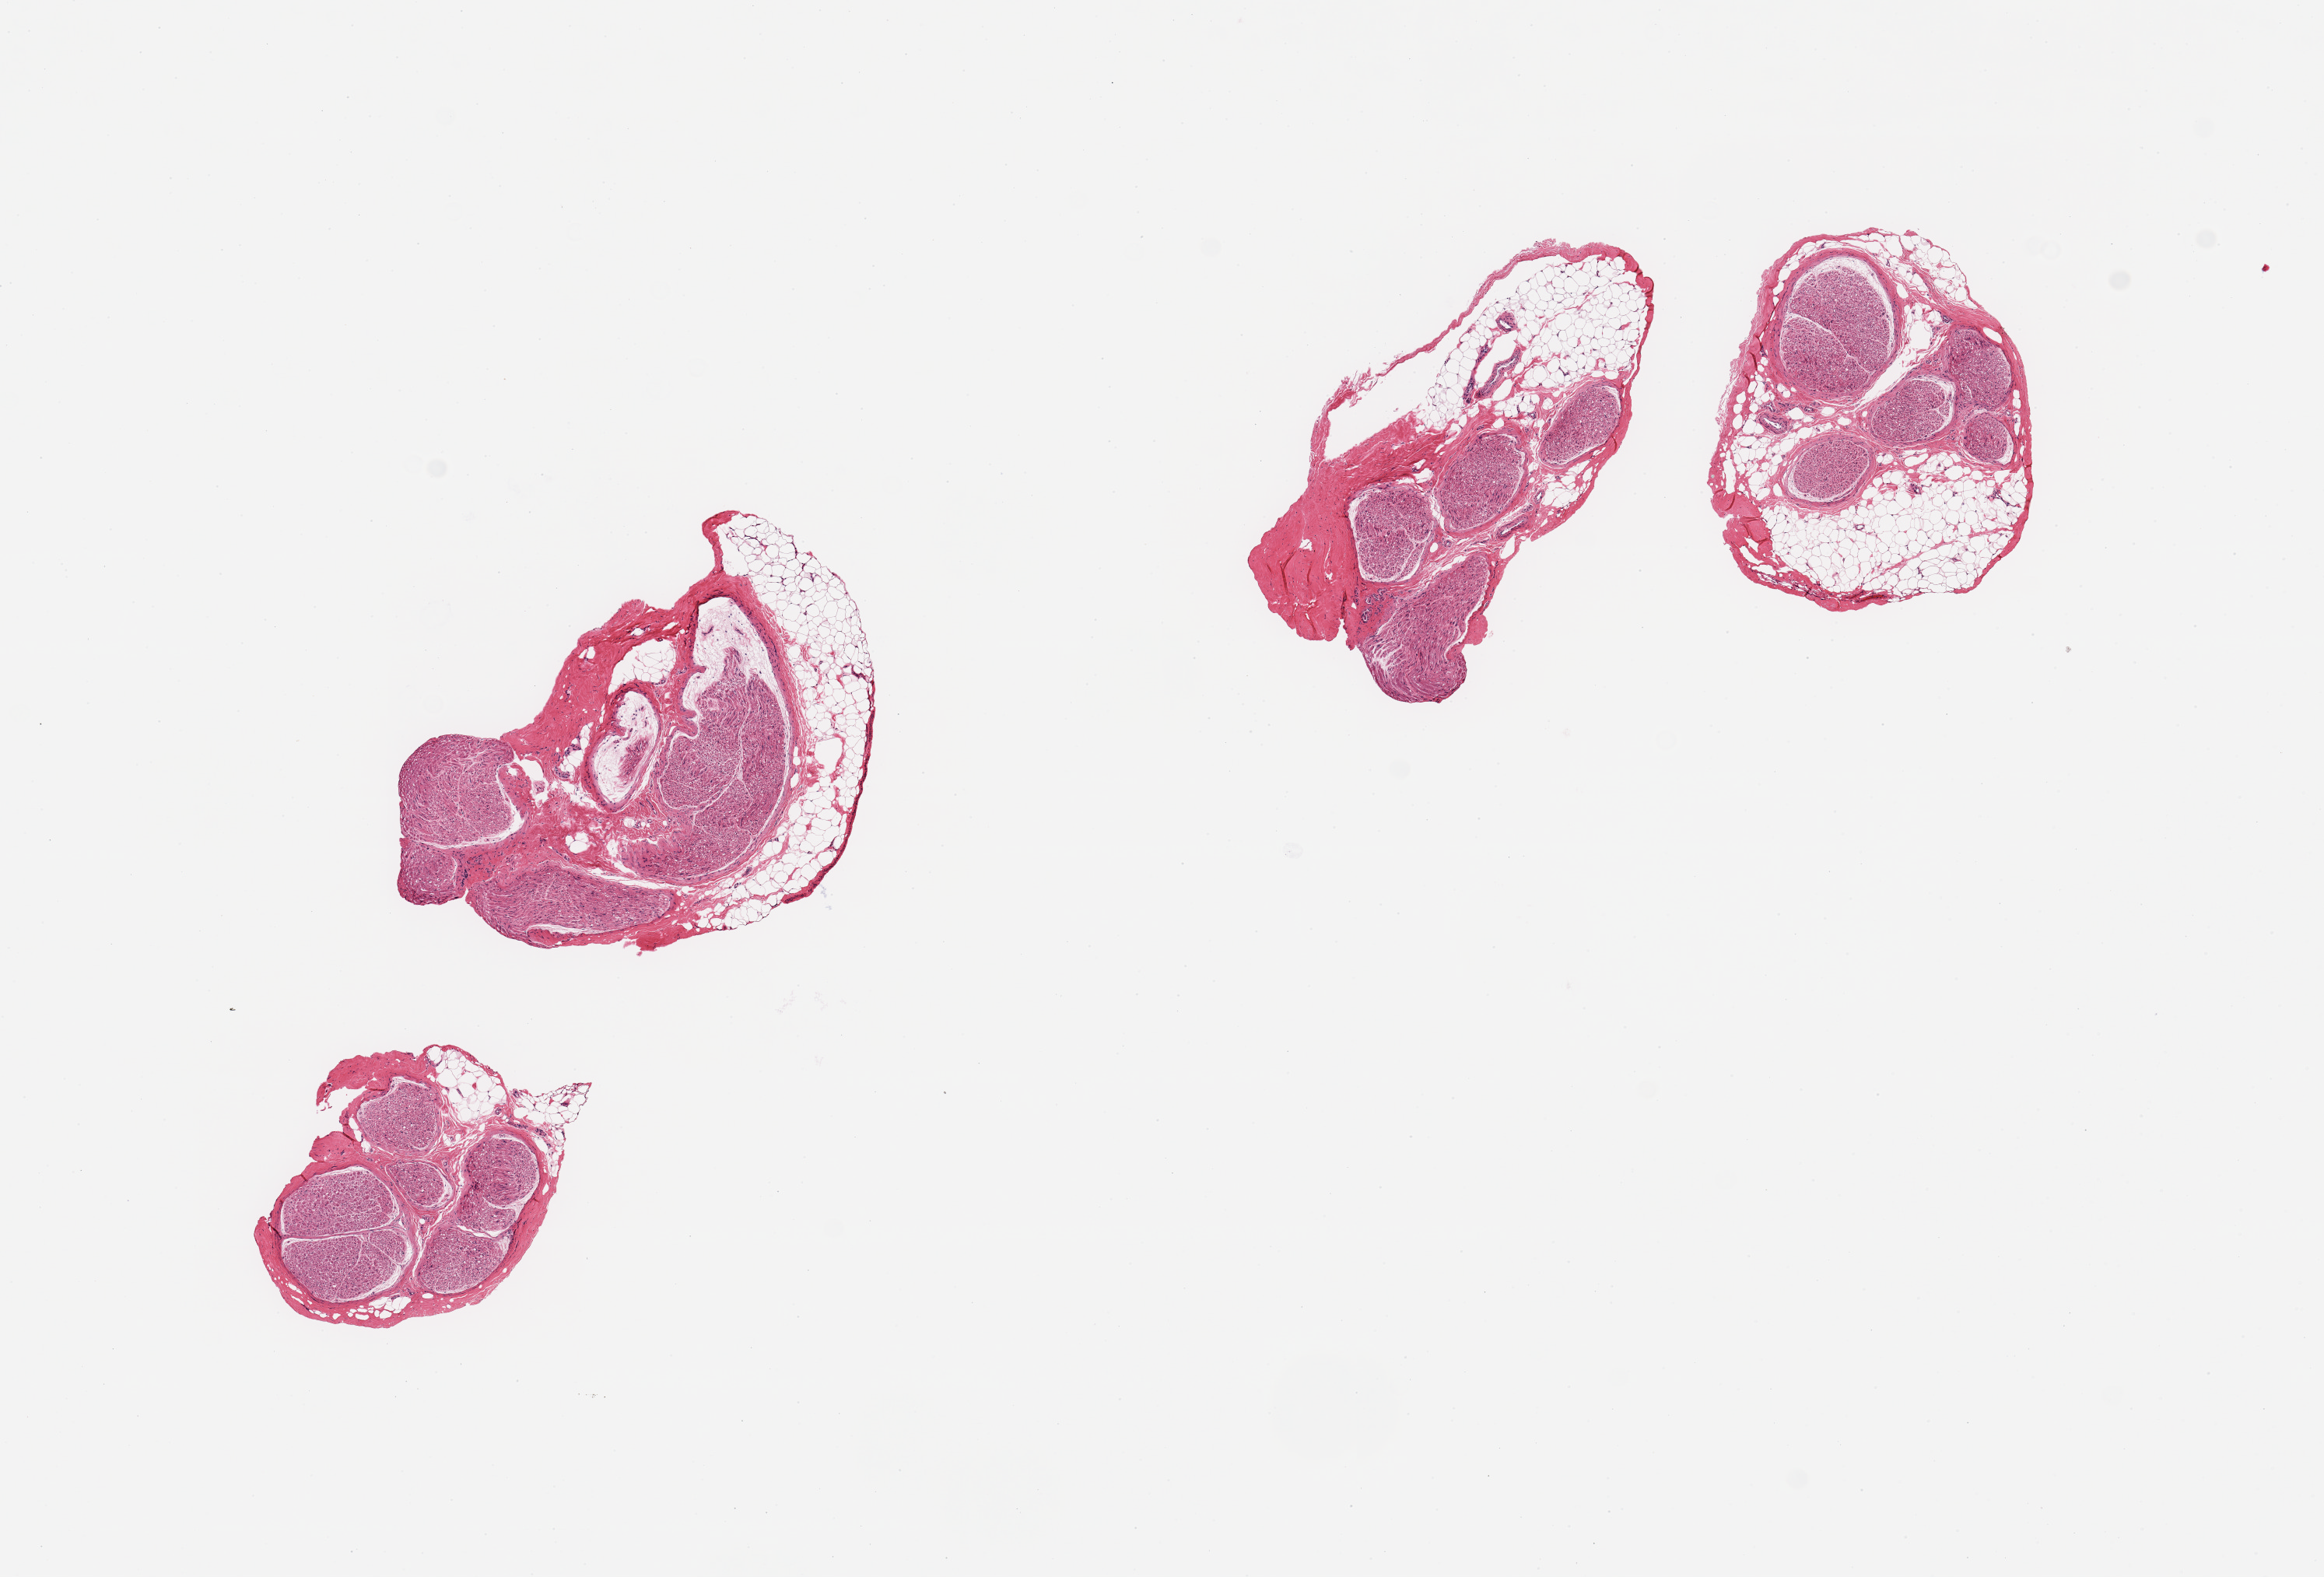
Whole-slide image, H&E stain — a low-resolution overview of the entire scanned area, about 11.8 x 8.0 mm (acquisition: 20x scan); PAXgene-fixed, paraffin-embedded tissue; sampled site (target tissue): tibial nerve; tissue donor sample. Donor: female.
• reviewer comment on this tissue sample: 4 pieces; nerve with up to 0.7mm attached fat (10-50%)